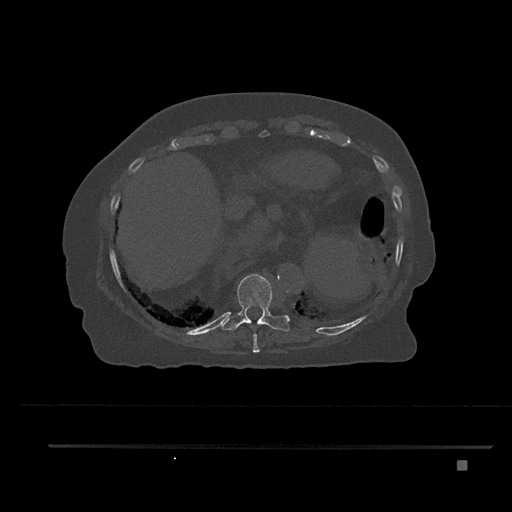
CT including the spine, one axial slice; slice 364 of 797 in the series (ordered by position); 120 kVp; bone window (W 1800 / L 400 HU); 0.5 mm slice thickness; 512 × 512 image matrix. Female patient, age 76 years. From the clinical record (not read from this slice): primary cancer: lung.
Structures marked on this image (semi-automatically segmented with operator editing):
- T10 vertebra: bounding box <220,274,290,332> (left, top, right, bottom; pixels)
- T9 vertebra: <252,333,260,353>